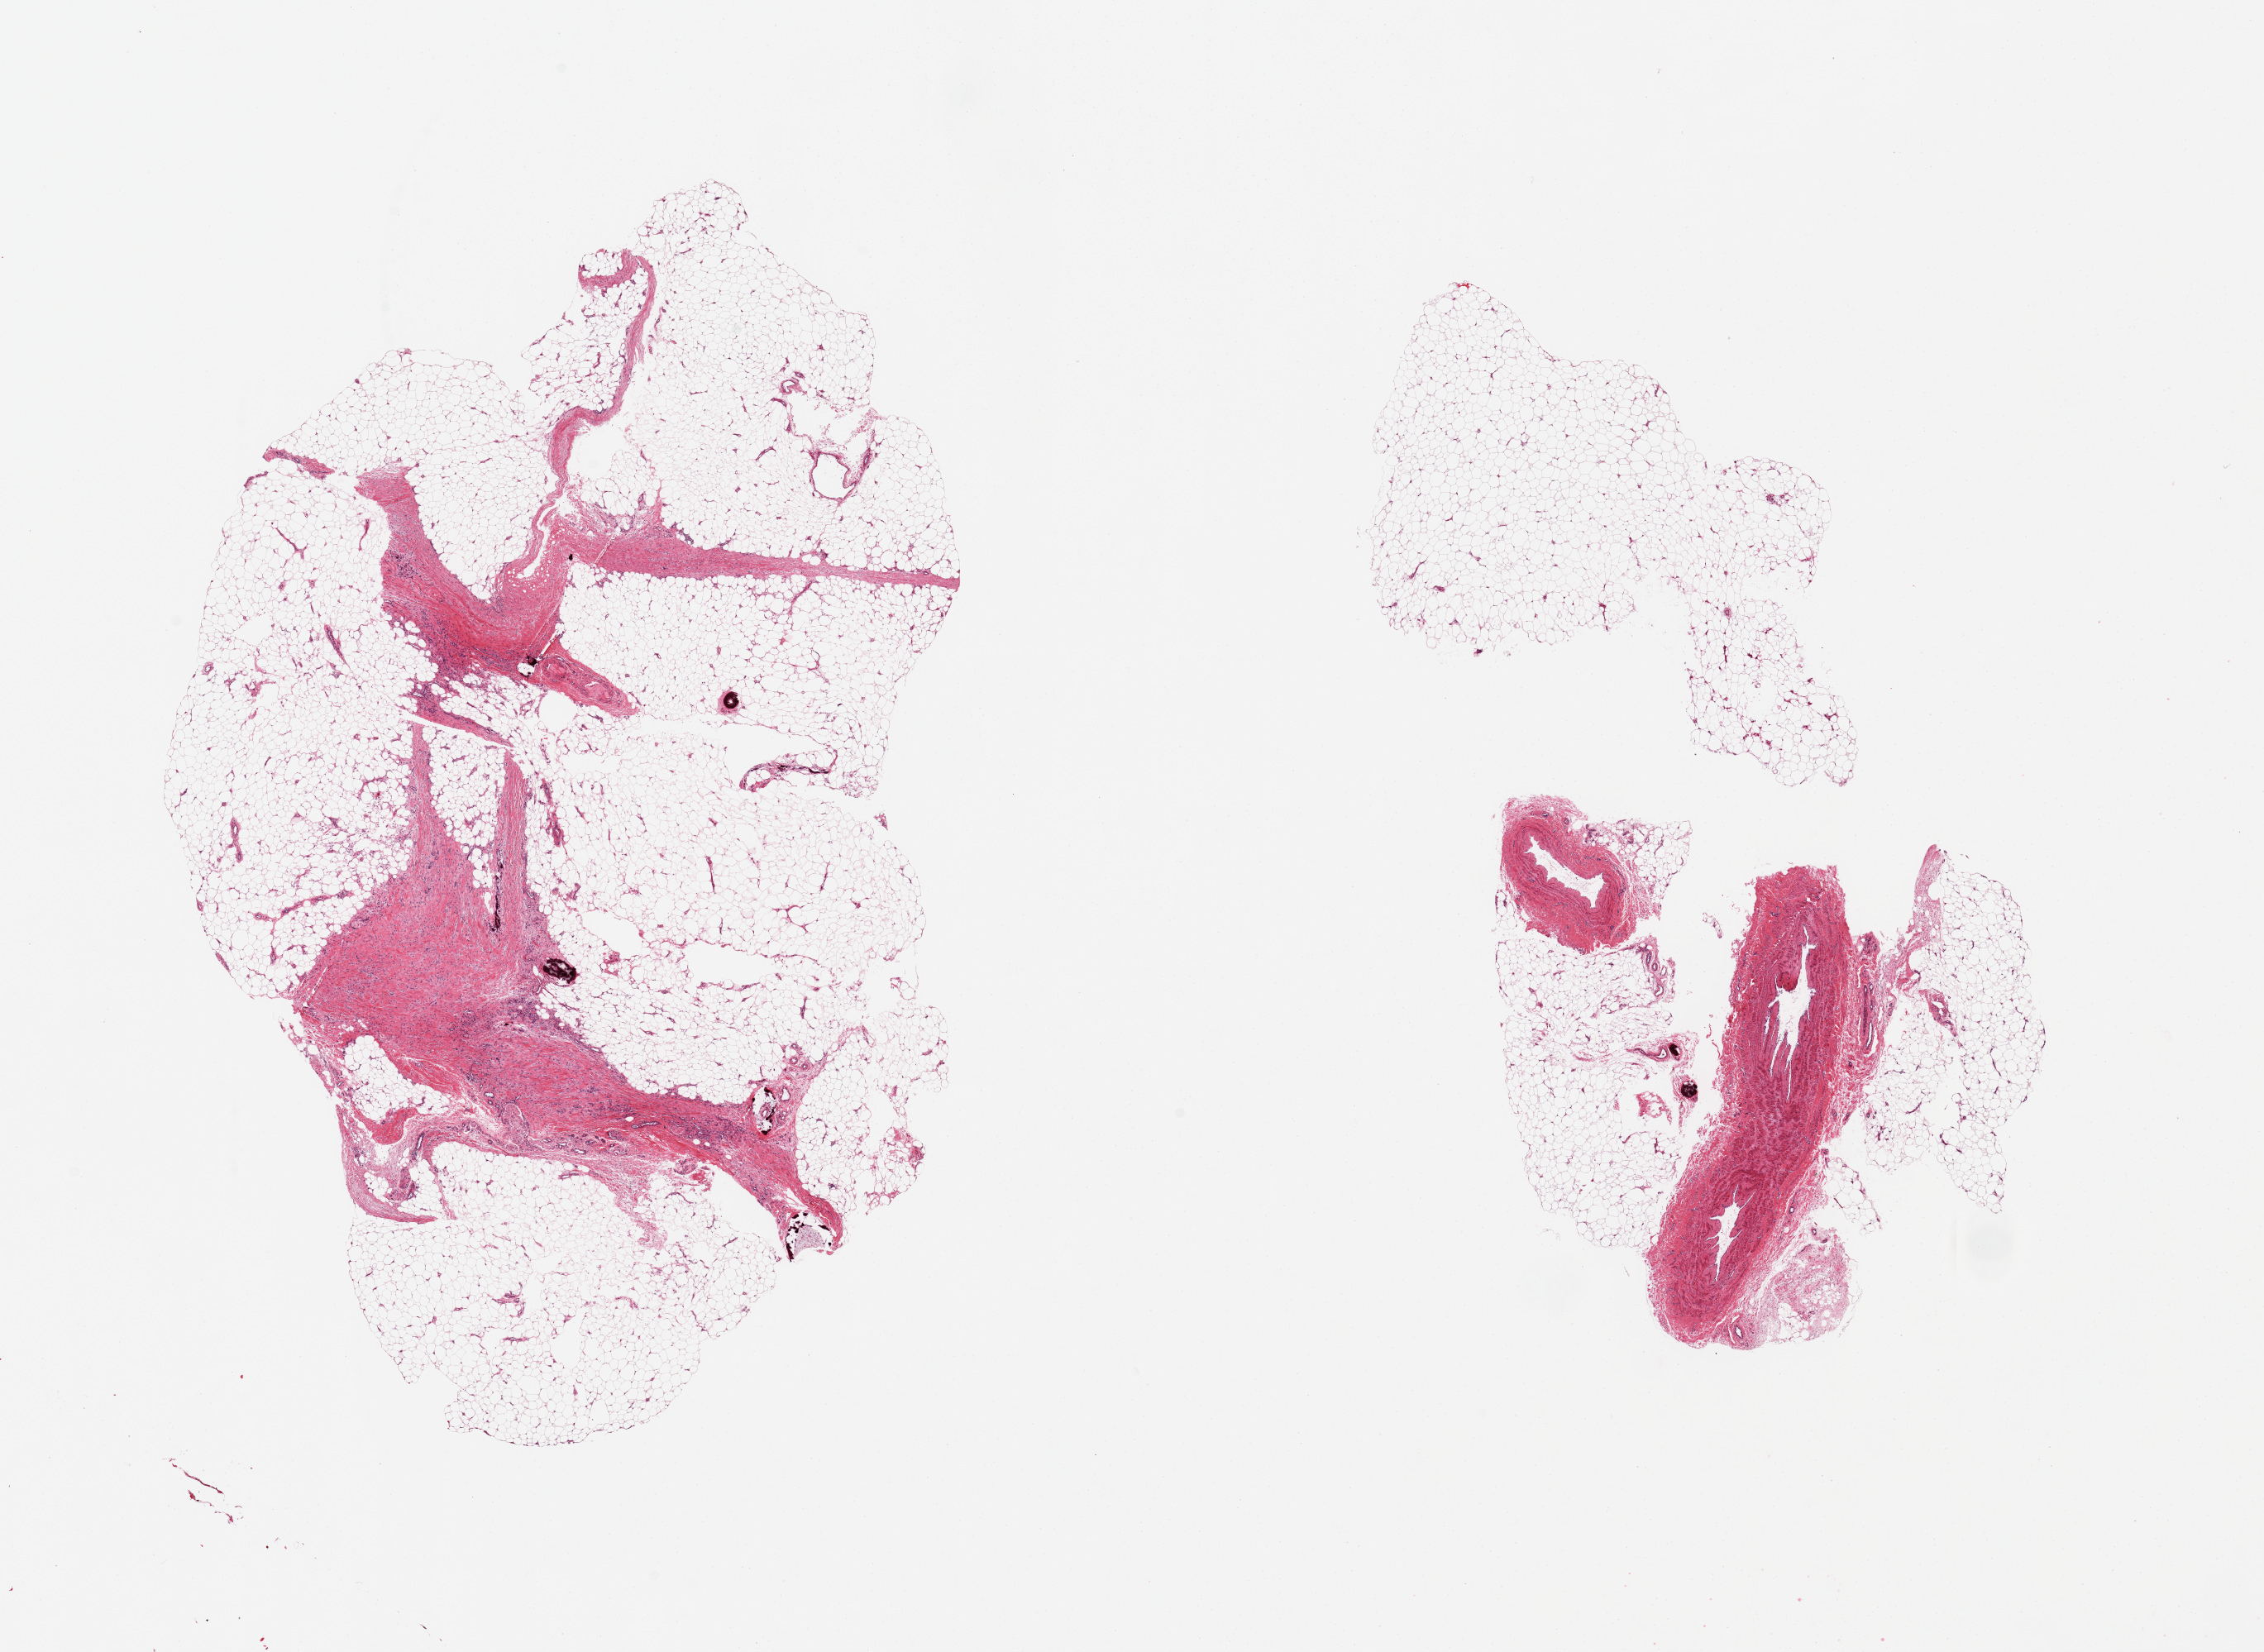
Haematoxylin and eosin whole-slide image, shown as a low-resolution overview of the whole scanned area (about 21.7 x 15.8 mm, from a 20x scan); PAXgene-fixed paraffin-embedded (PFPE) section; target tissue: adipose tissue; donor tissue sample. Female donor.
* review note (as recorded): 3 pieces; large blood vessels and fibrous stroma comprise 30% of overall area